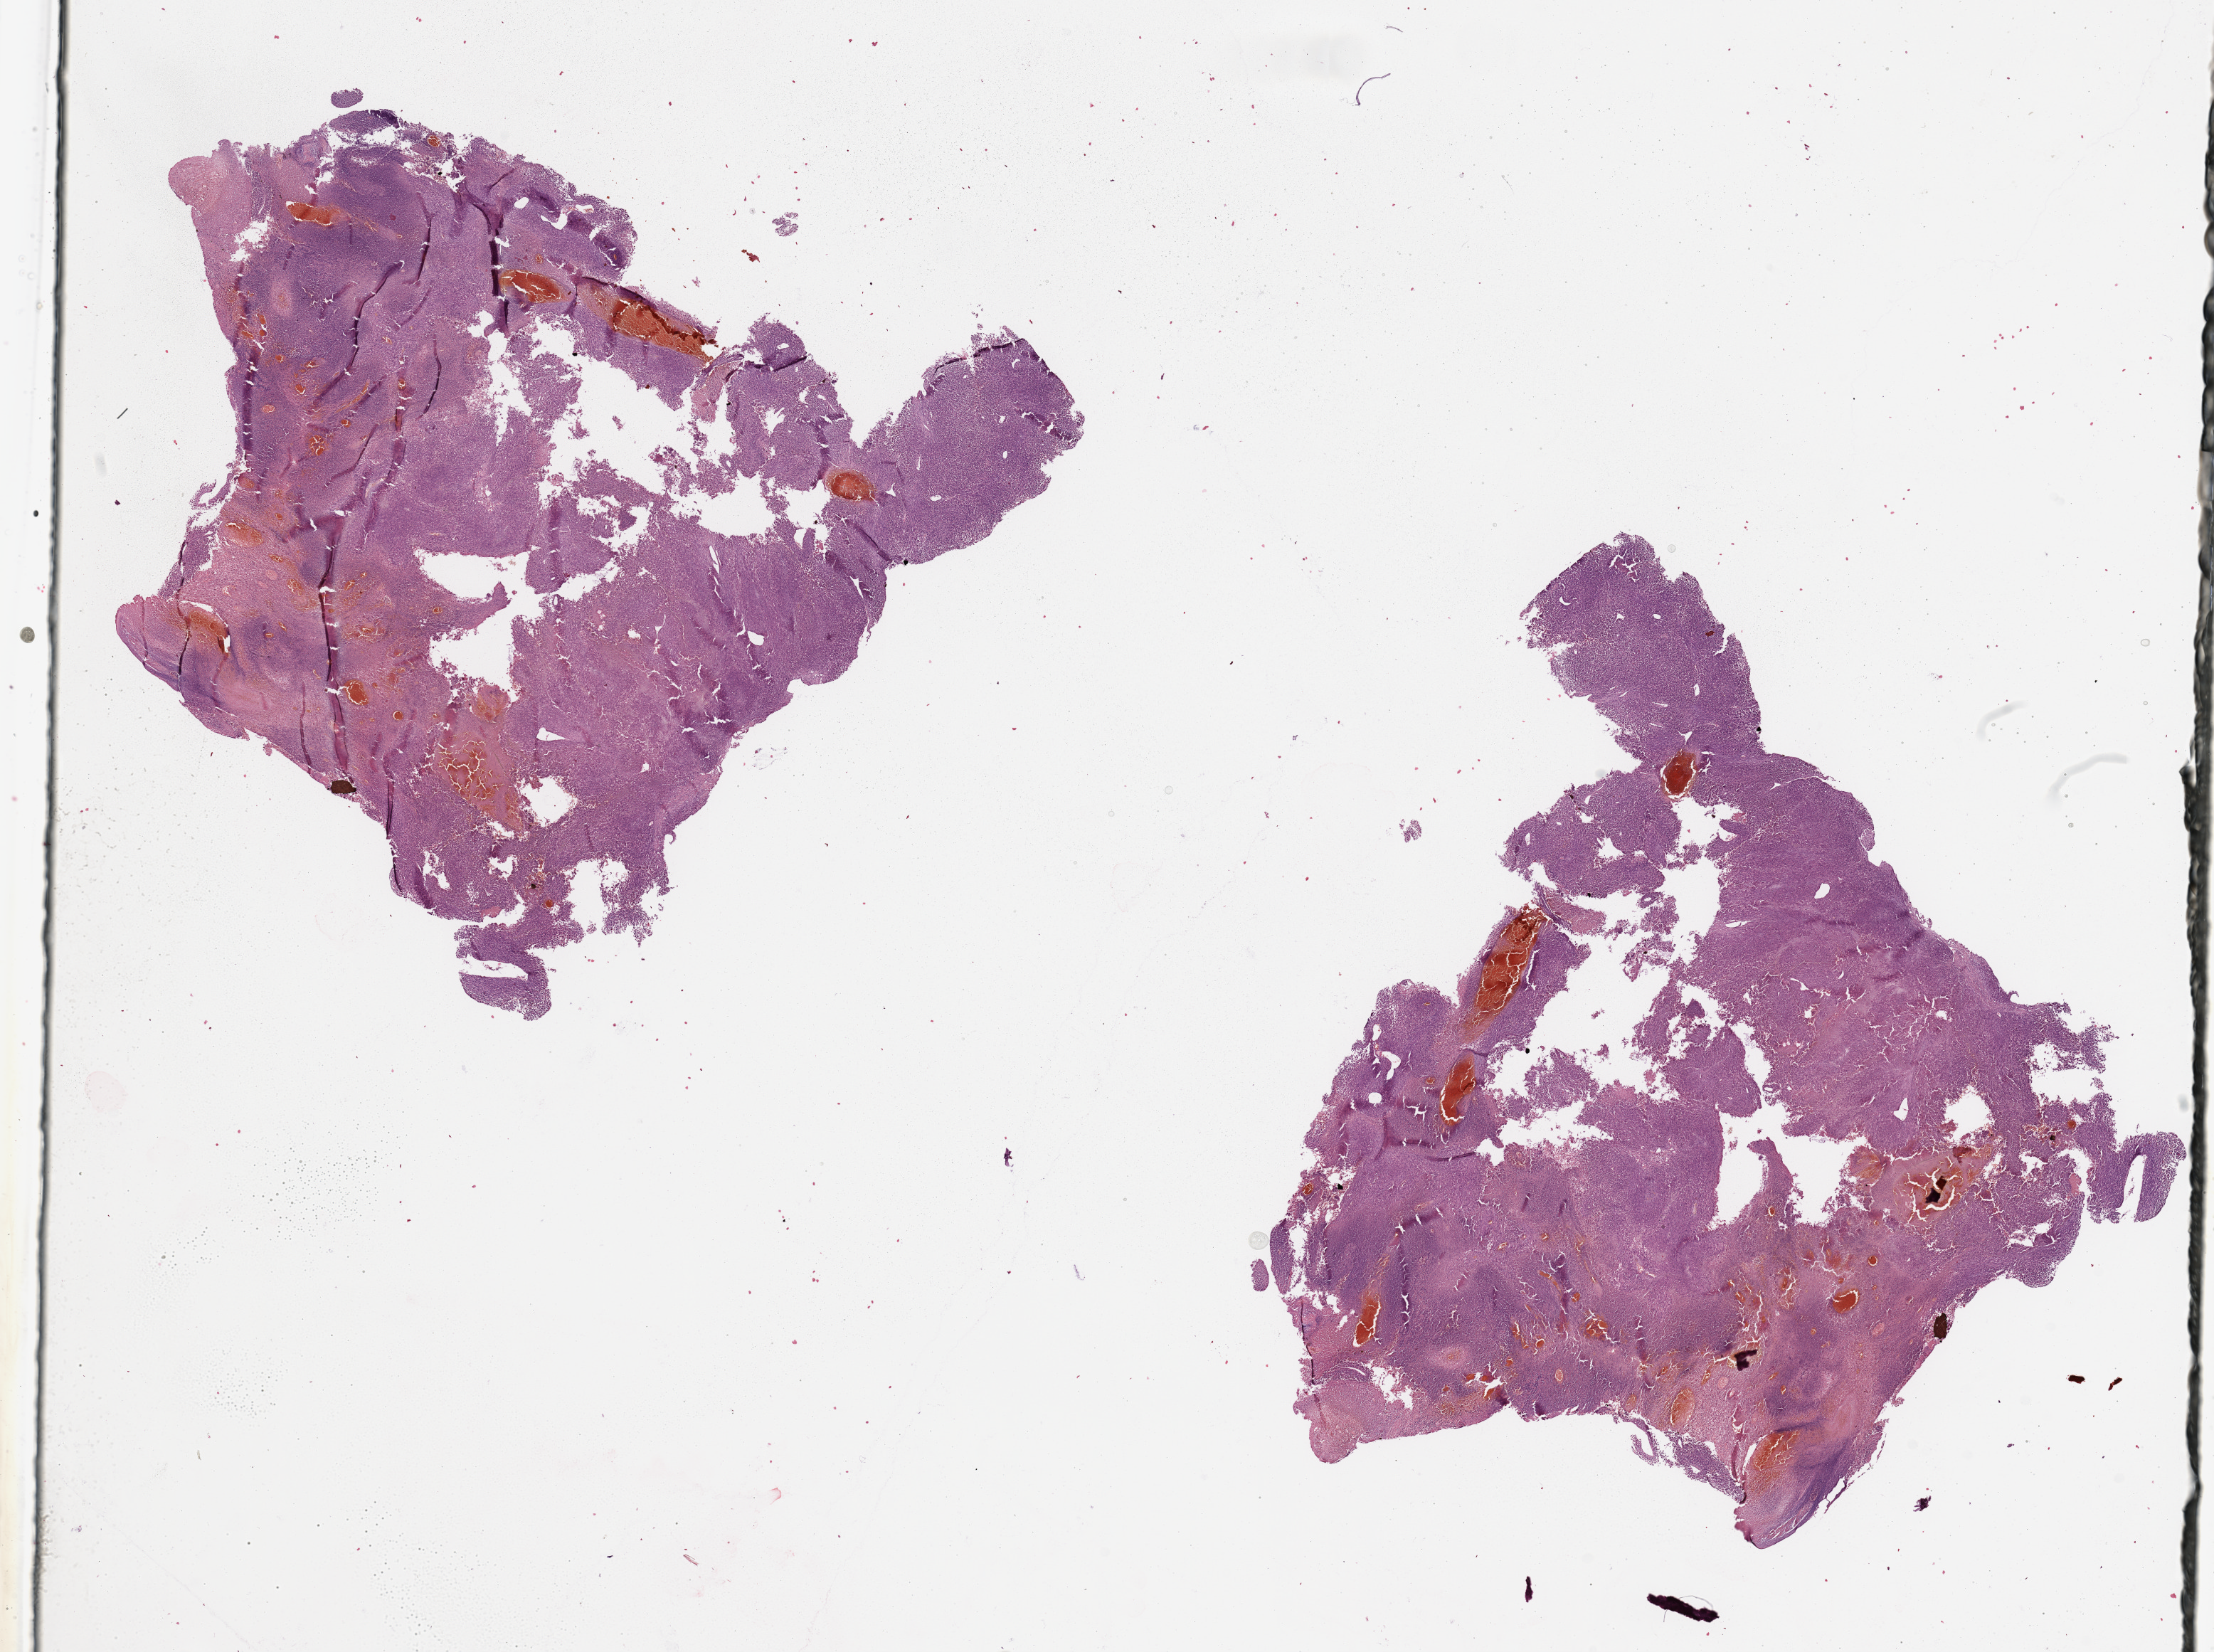
Digitized Hematoxylin and eosin (H&E) stained tissue section (whole slide), low-resolution overview of the scanned area, about 24.6 x 18.4 mm, melanoma tumour tissue; sampled site not recorded. Patient: male, age 75 years.
• AJCC pathologic stage: IIC
• primary tumour site (as recorded): trunk
• diagnosis: Malignant melanoma, NOS